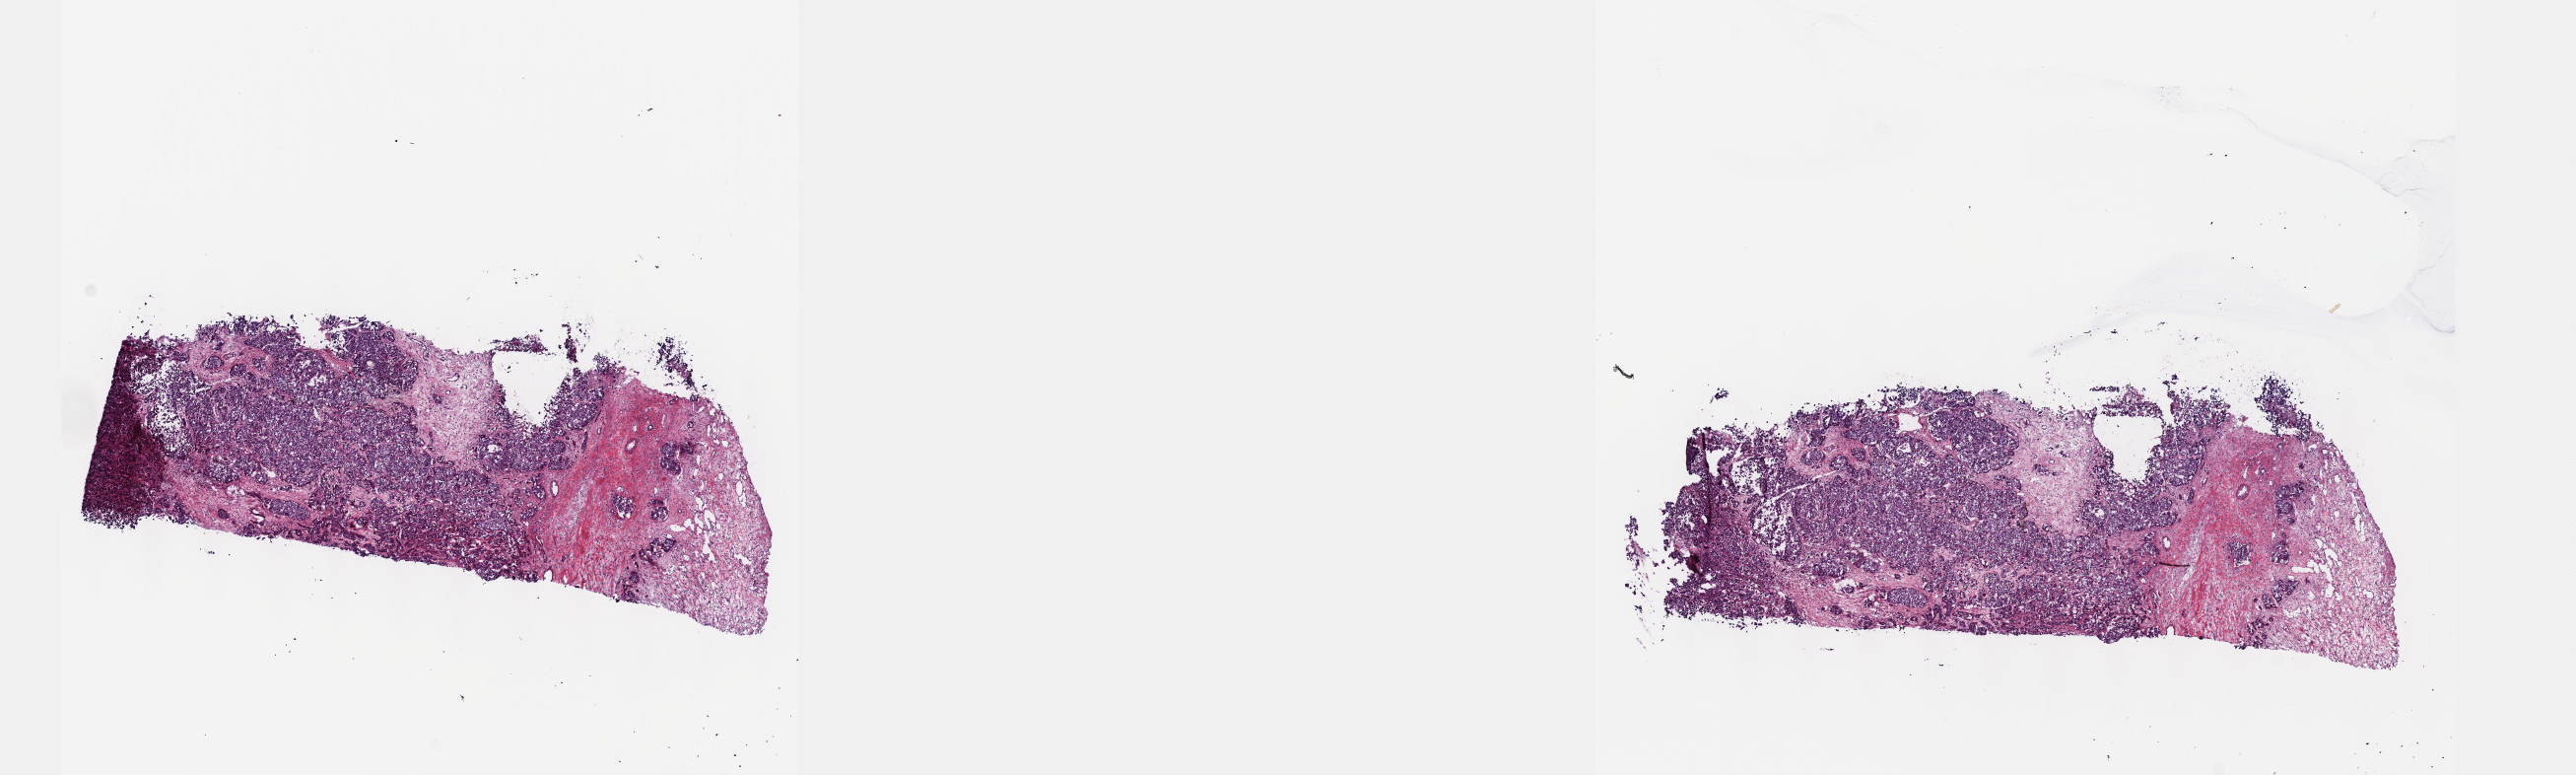
Digitized Hematoxylin and eosin (H&E) stained tissue section (whole slide) — shown as a low-resolution overview of the whole scanned area (about 21.1 x 6.4 mm); frozen section from the top of the tissue portion; primary tumour sample from the liver. Patient: female, age at initial diagnosis 48 years.
Histologic diagnosis: Hepatocellular carcinoma, NOS.